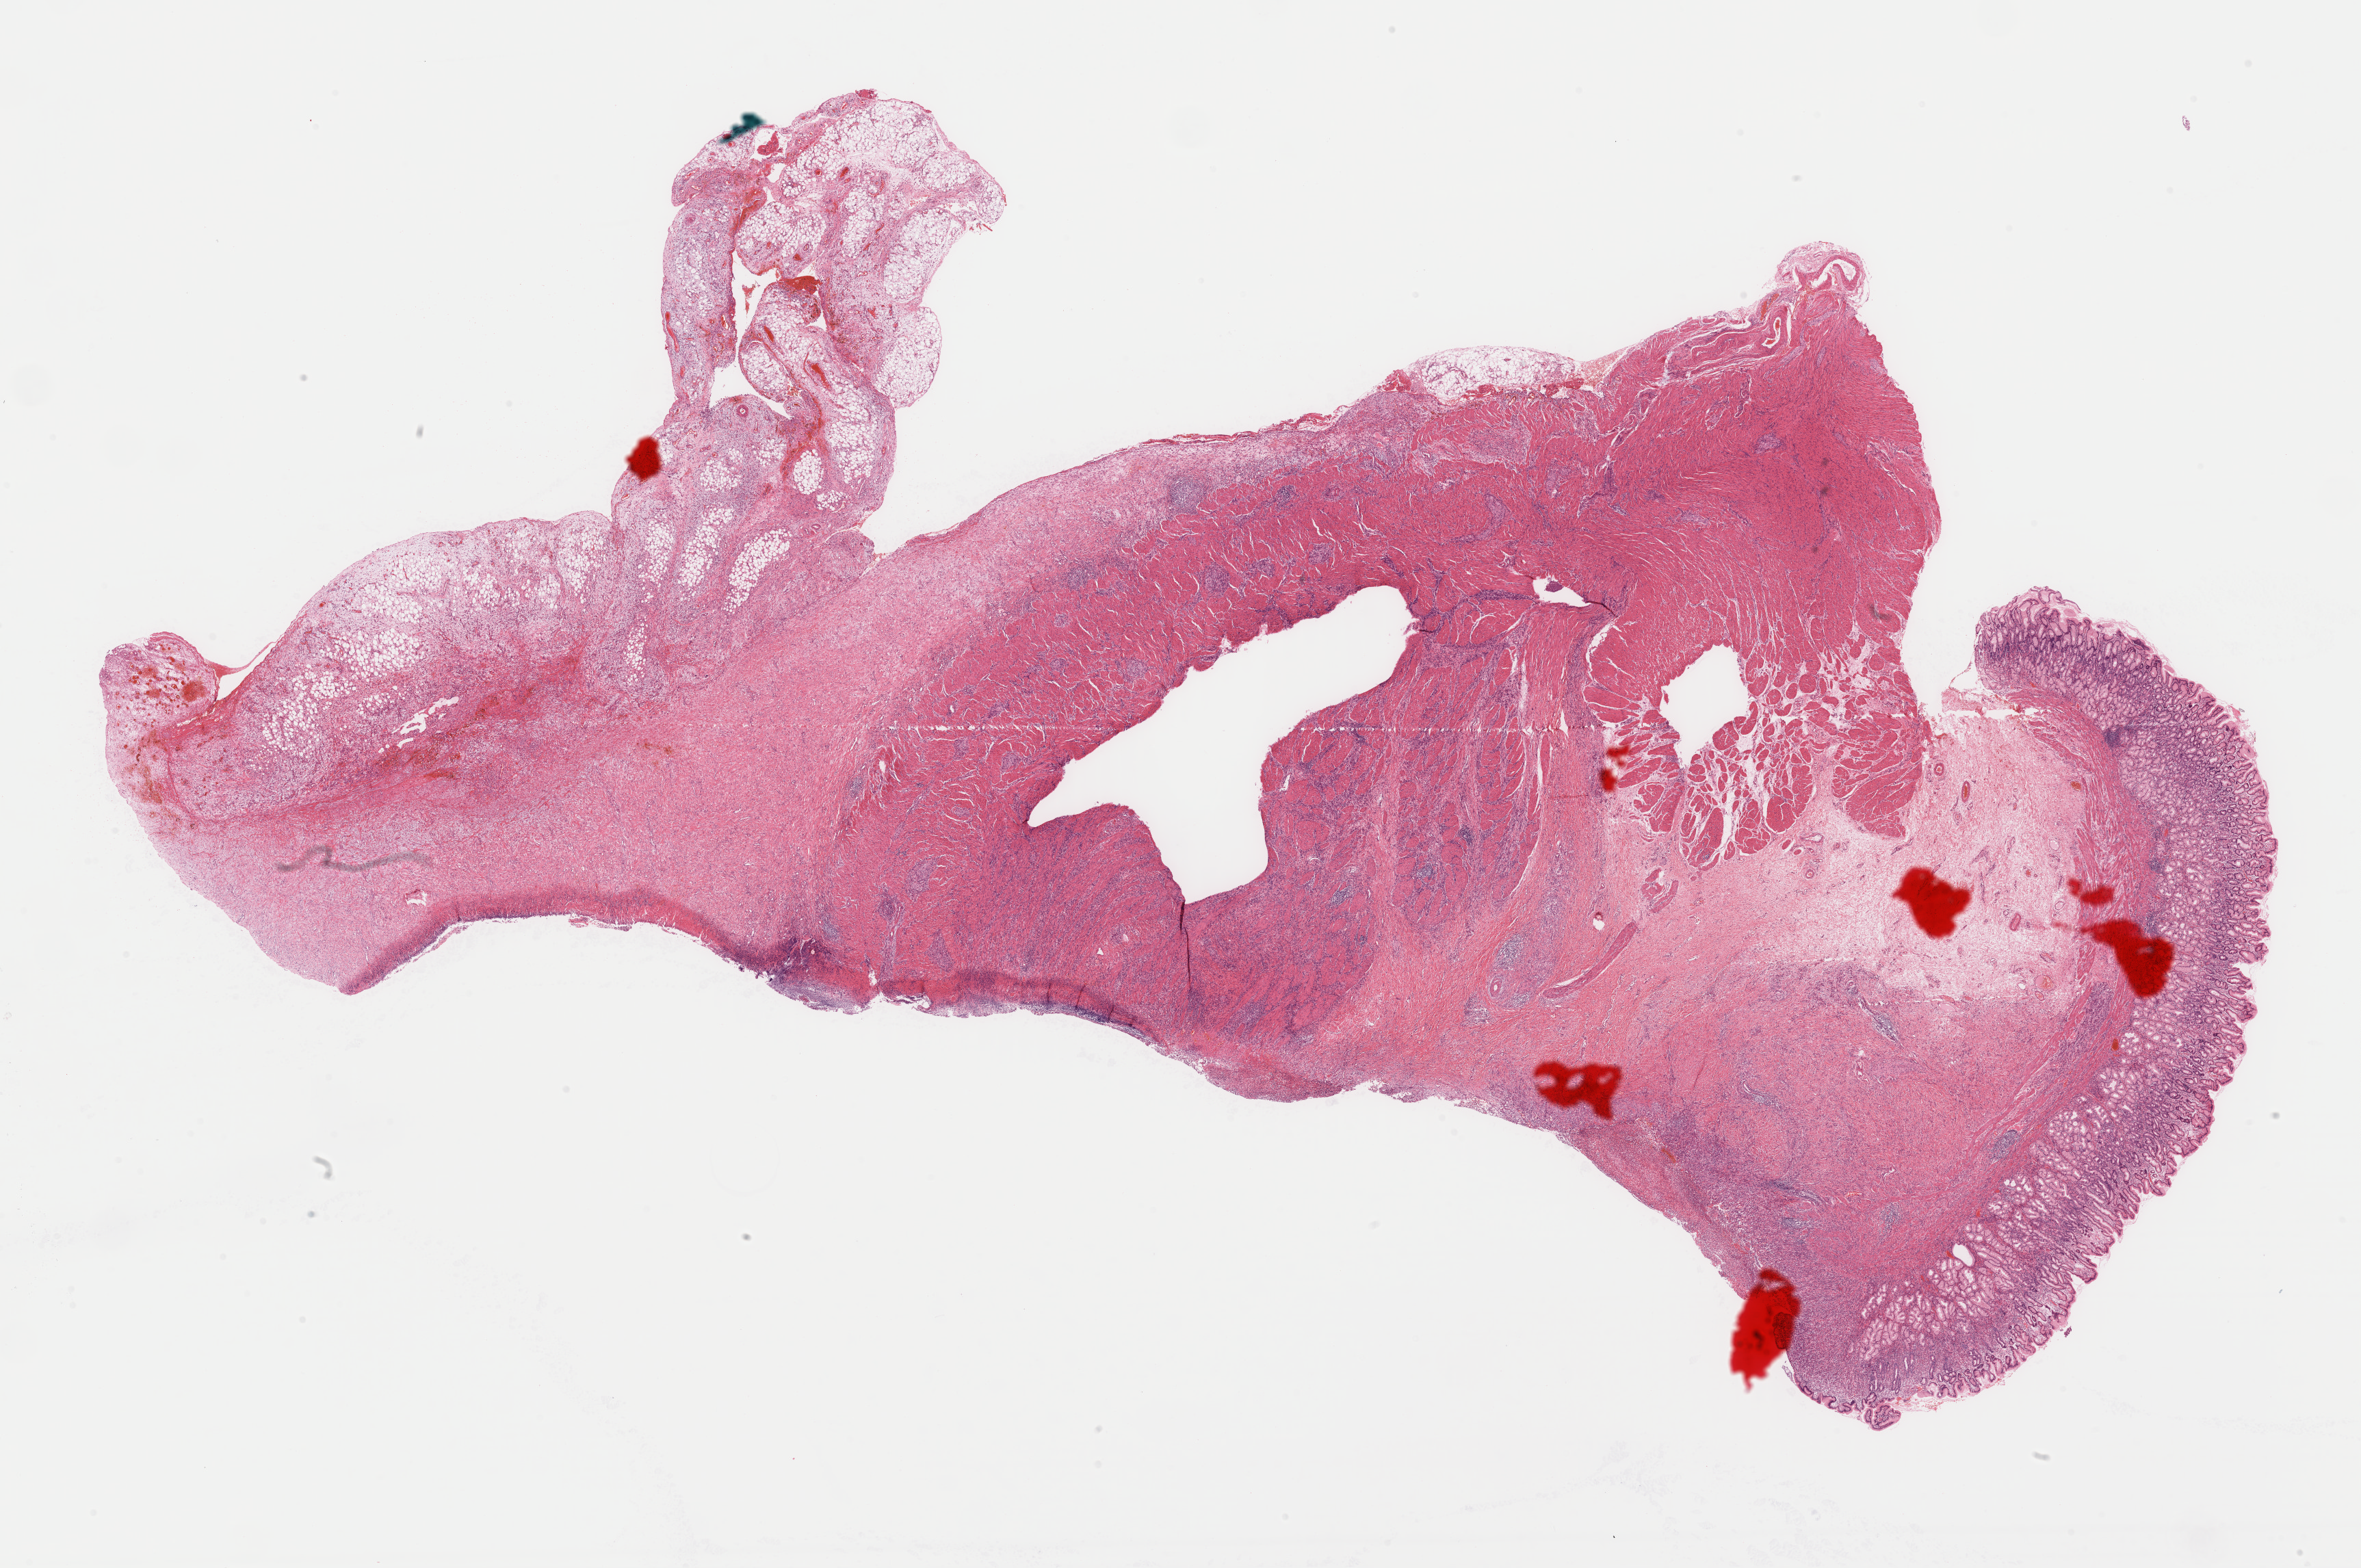
Digitized Hematoxylin and eosin (H&E) stained tissue section (whole slide) — a low-resolution overview of the entire scanned area, about 27.3 x 18.1 mm; formalin-fixed paraffin-embedded (FFPE) diagnostic section; sample: primary tumour, stomach. Male, age 47 years at initial diagnosis. Histologic grade: G3 (poorly differentiated).
• lymph nodes positive (case pathology): 3 of 9 examined
• AJCC pathologic stage: IIIB
• histologic diagnosis: Carcinoma, diffuse type (gastric antrum)